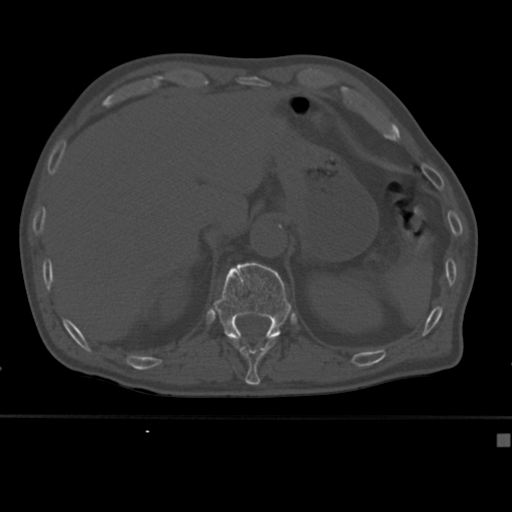
CT including the spine, one axial slice. Position 198 of 430 along the scan axis. Reconstruction kernel Br40s. 120 kVp. Bone window (W 1800 / L 400 HU). 1.5 mm slice thickness. 512 × 512 image matrix, field of view 337 × 337 mm. Patient: male, 64 years. Case-level facts recorded for this patient, not image findings: primary cancer: uterus; vertebrae with lytic lesions (as recorded): T1, T4, T5, T7, L5.
Annotated regions visible in this slice (semi-automatic segmentation, software-assisted and operator-edited):
- T11 vertebra: bounding box (x1, y1, x2, y2) in pixels: (232, 337, 276, 382)
- T12 vertebra: (214, 262, 292, 341)